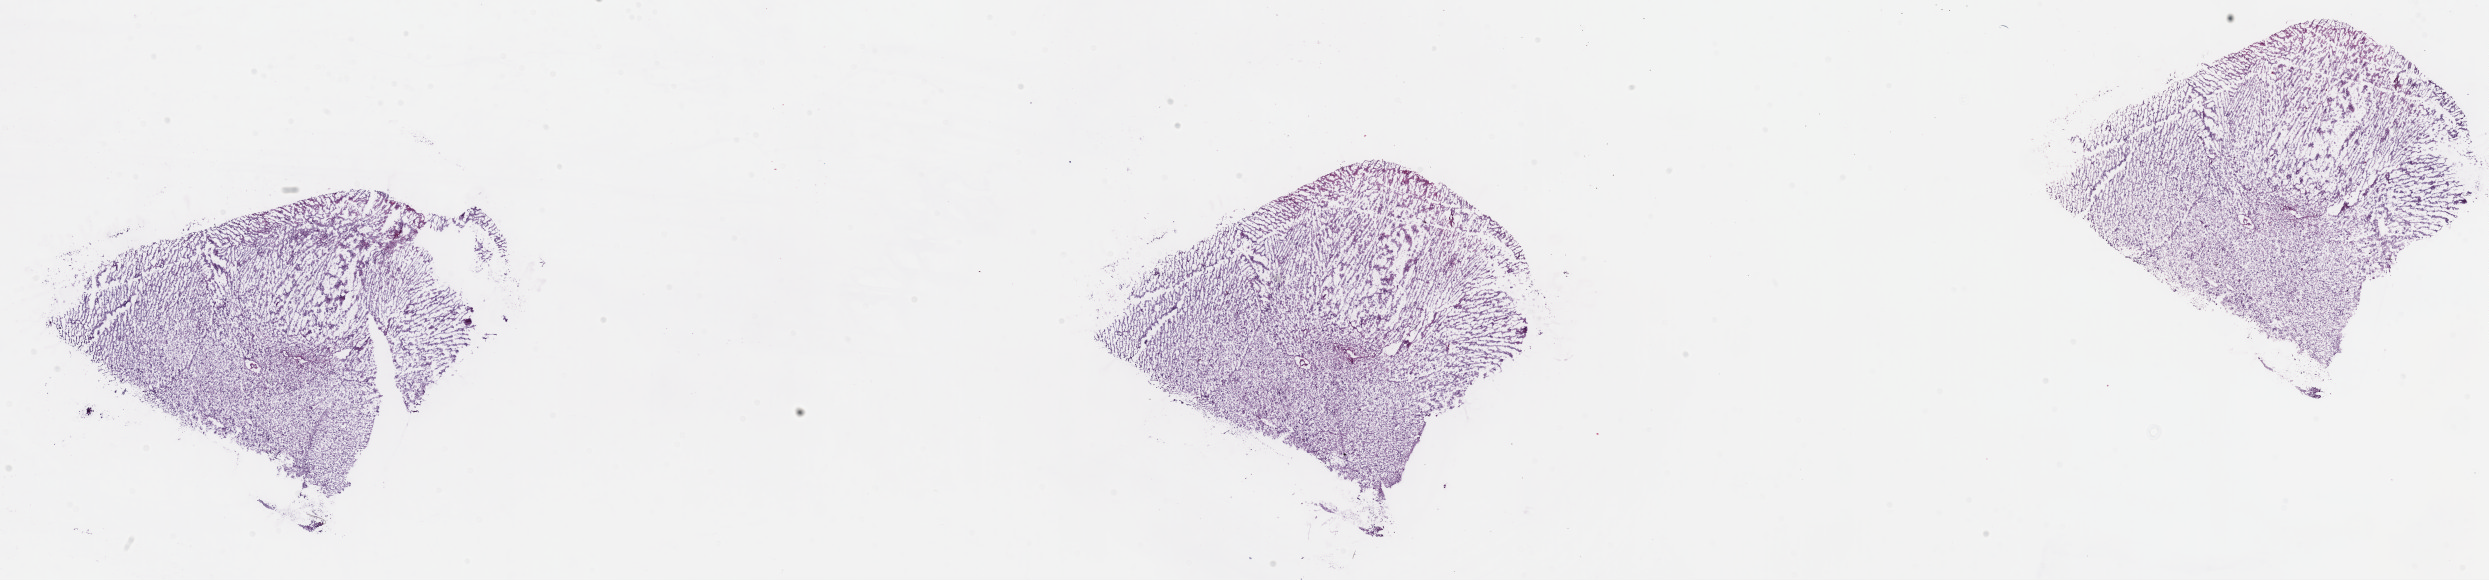
Digitized Hematoxylin and eosin (H&E) stained tissue section (whole slide) — whole scanned area (about 40.3 x 9.4 mm, from a 40x scan) shown as a low-resolution overview. Frozen section from the top of the tissue portion. Primary tumour sample from the brain. Male patient; age at initial diagnosis 24 years. Histologic grade: G2 (moderately differentiated). Slide review estimates, as recorded: tumour cells 40%, tumour nuclei 85%, normal cells 10%, stromal cells 50%, necrosis 0%. Inflammatory infiltration, as recorded: lymphocyte infiltration 0%, monocyte infiltration 0%, neutrophil infiltration 0%.
- diagnosis: Astrocytoma, NOS (cerebrum)